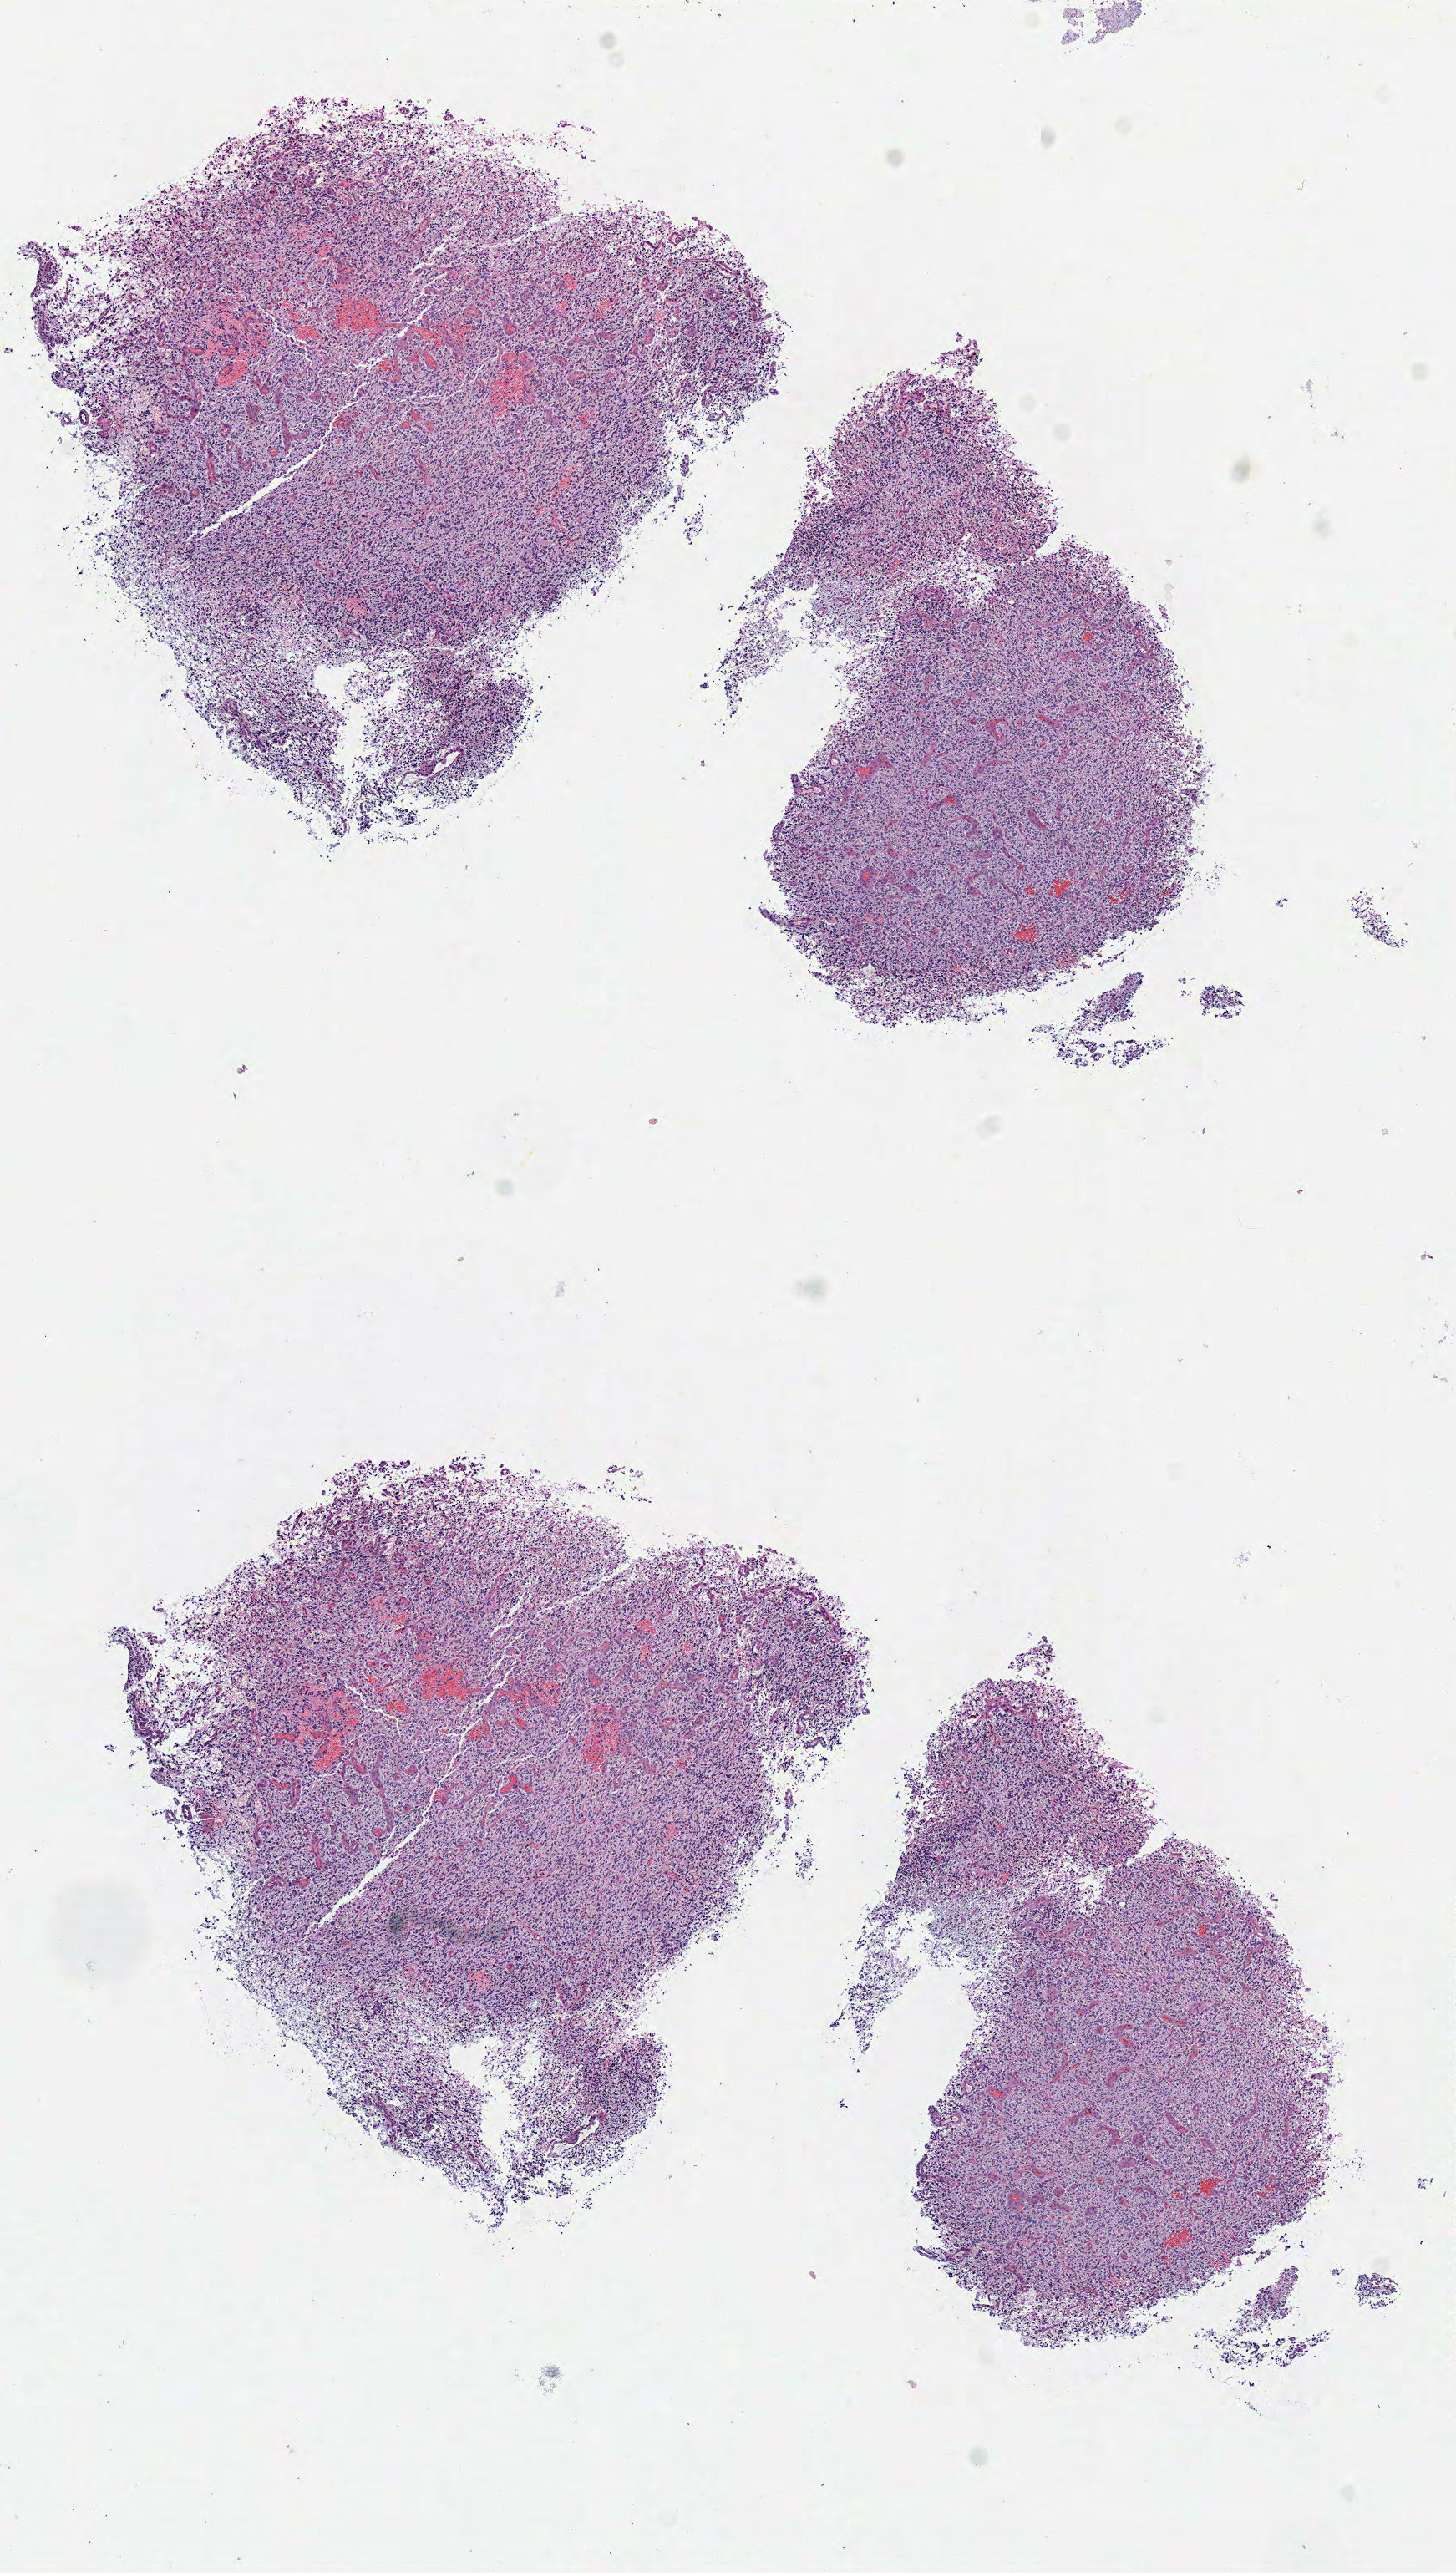
Digitized H&E-stained tissue section (whole slide) — low-resolution overview of the scanned area, about 6.9 x 12.1 mm, frozen section from the top of the tissue portion, brain, primary tumour sample. Female, age 44 years at initial diagnosis. Pathologist review of this section (percent, as recorded): tumour cells 95%, tumour nuclei 85%.
Diagnosis: Glioblastoma.